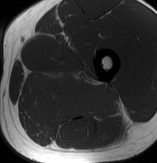
MRI of an extremity soft-tissue mass, one axial slice; slice 46 of 70 in the series (ordered by position); MR volume resampled by the dataset authors to the PET/CT grid (not the native acquisition matrix); 3.27 mm slice thickness; 157 × 163 image matrix, field of view 153 × 159 mm. Male patient. From the clinical record (not read from this slice): histological type: extraskeletal osteosarcoma; grade: high; site of the primary tumour: left adductur.
Outlined on this slice (expert contour drawn on MRI and transferred to this co-registered scan by the dataset authors):
- gross tumour volume (mass): bounding box (x1, y1, x2, y2) in pixels: (28, 65, 121, 123)